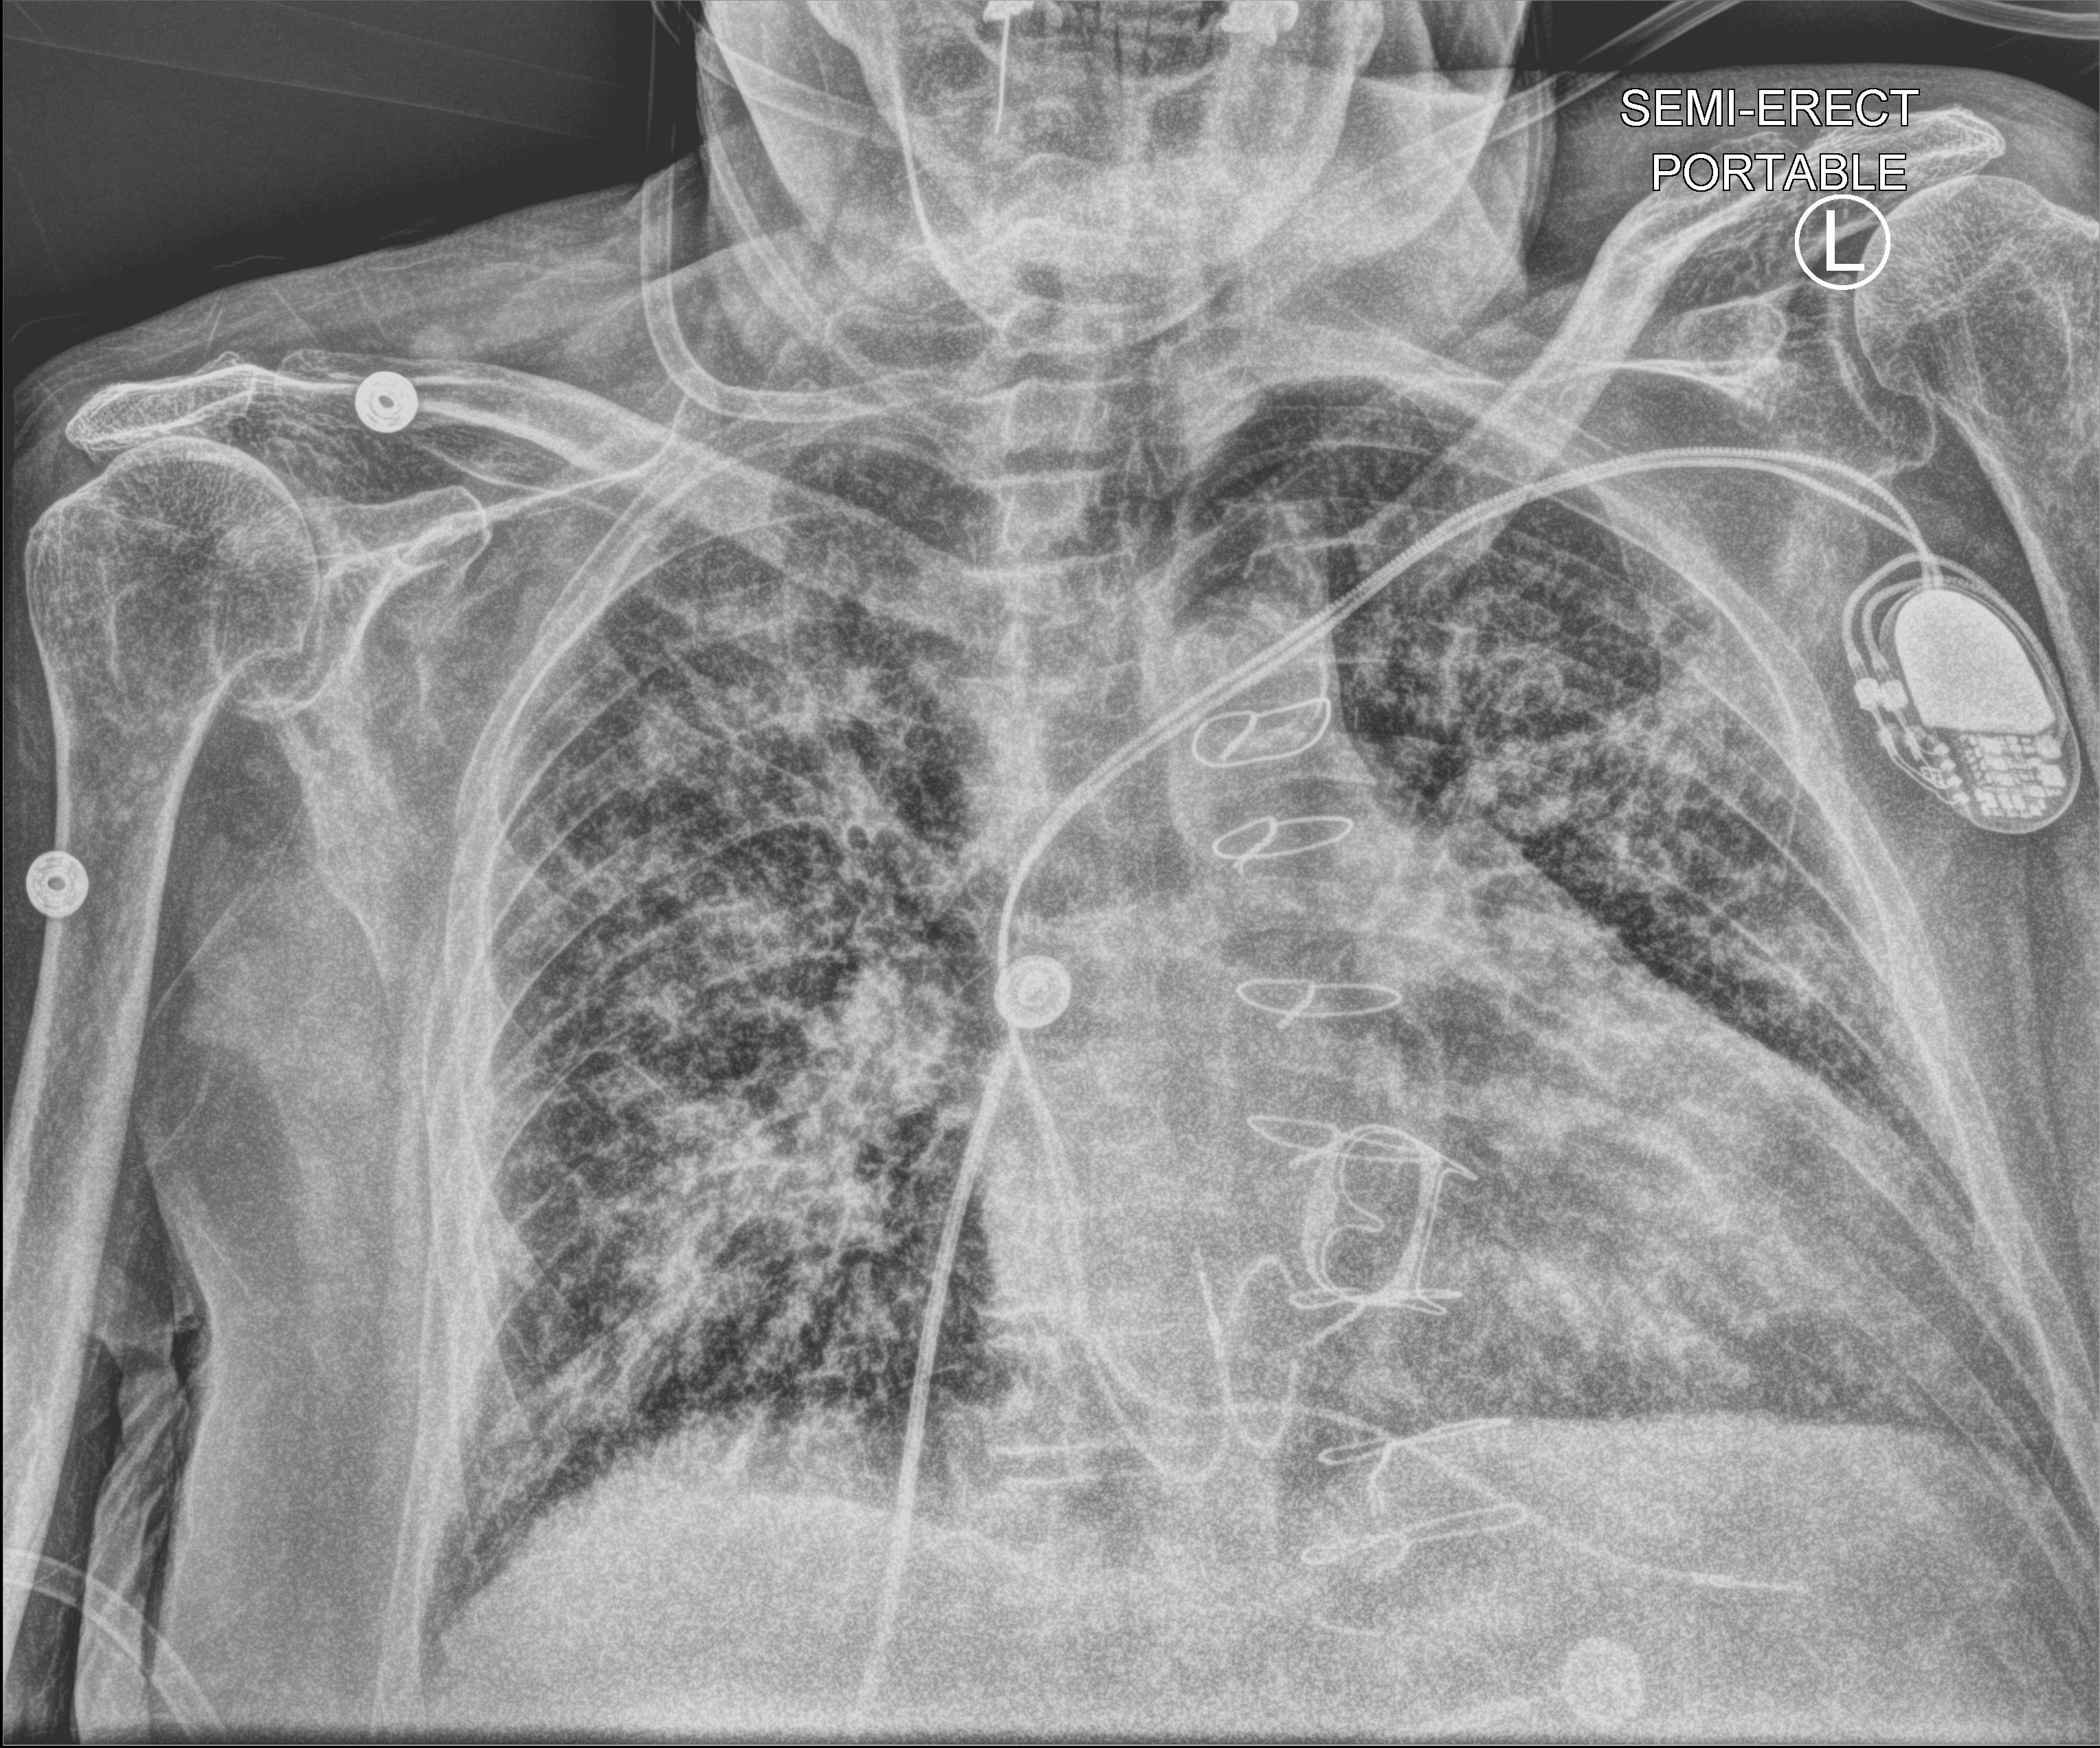
Bedside chest radiograph (computed radiography), anteroposterior (AP) projection. Male patient hospitalised with COVID-19, age 75–90 years.
From the hospital-stay record, not from the radiograph (when in the stay this image was taken is not recorded): hypertension (admission record): yes.